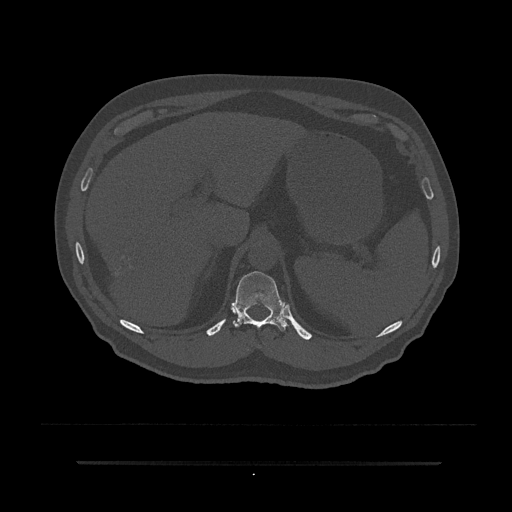
CT including the spine, one axial slice; slice 271 of 797 in the series (ordered by position); 120 kVp; bone window (W 1800 / L 400 HU); 512 × 512 image matrix. Male patient, age 59 years. From the clinical record (not read from this slice): primary cancer: bile ducts.
Annotated regions visible in this slice (semi-automatic segmentation, software-assisted and operator-edited):
- T11 vertebra: bounding box (x1, y1, x2, y2) in pixels: (232, 271, 289, 332)